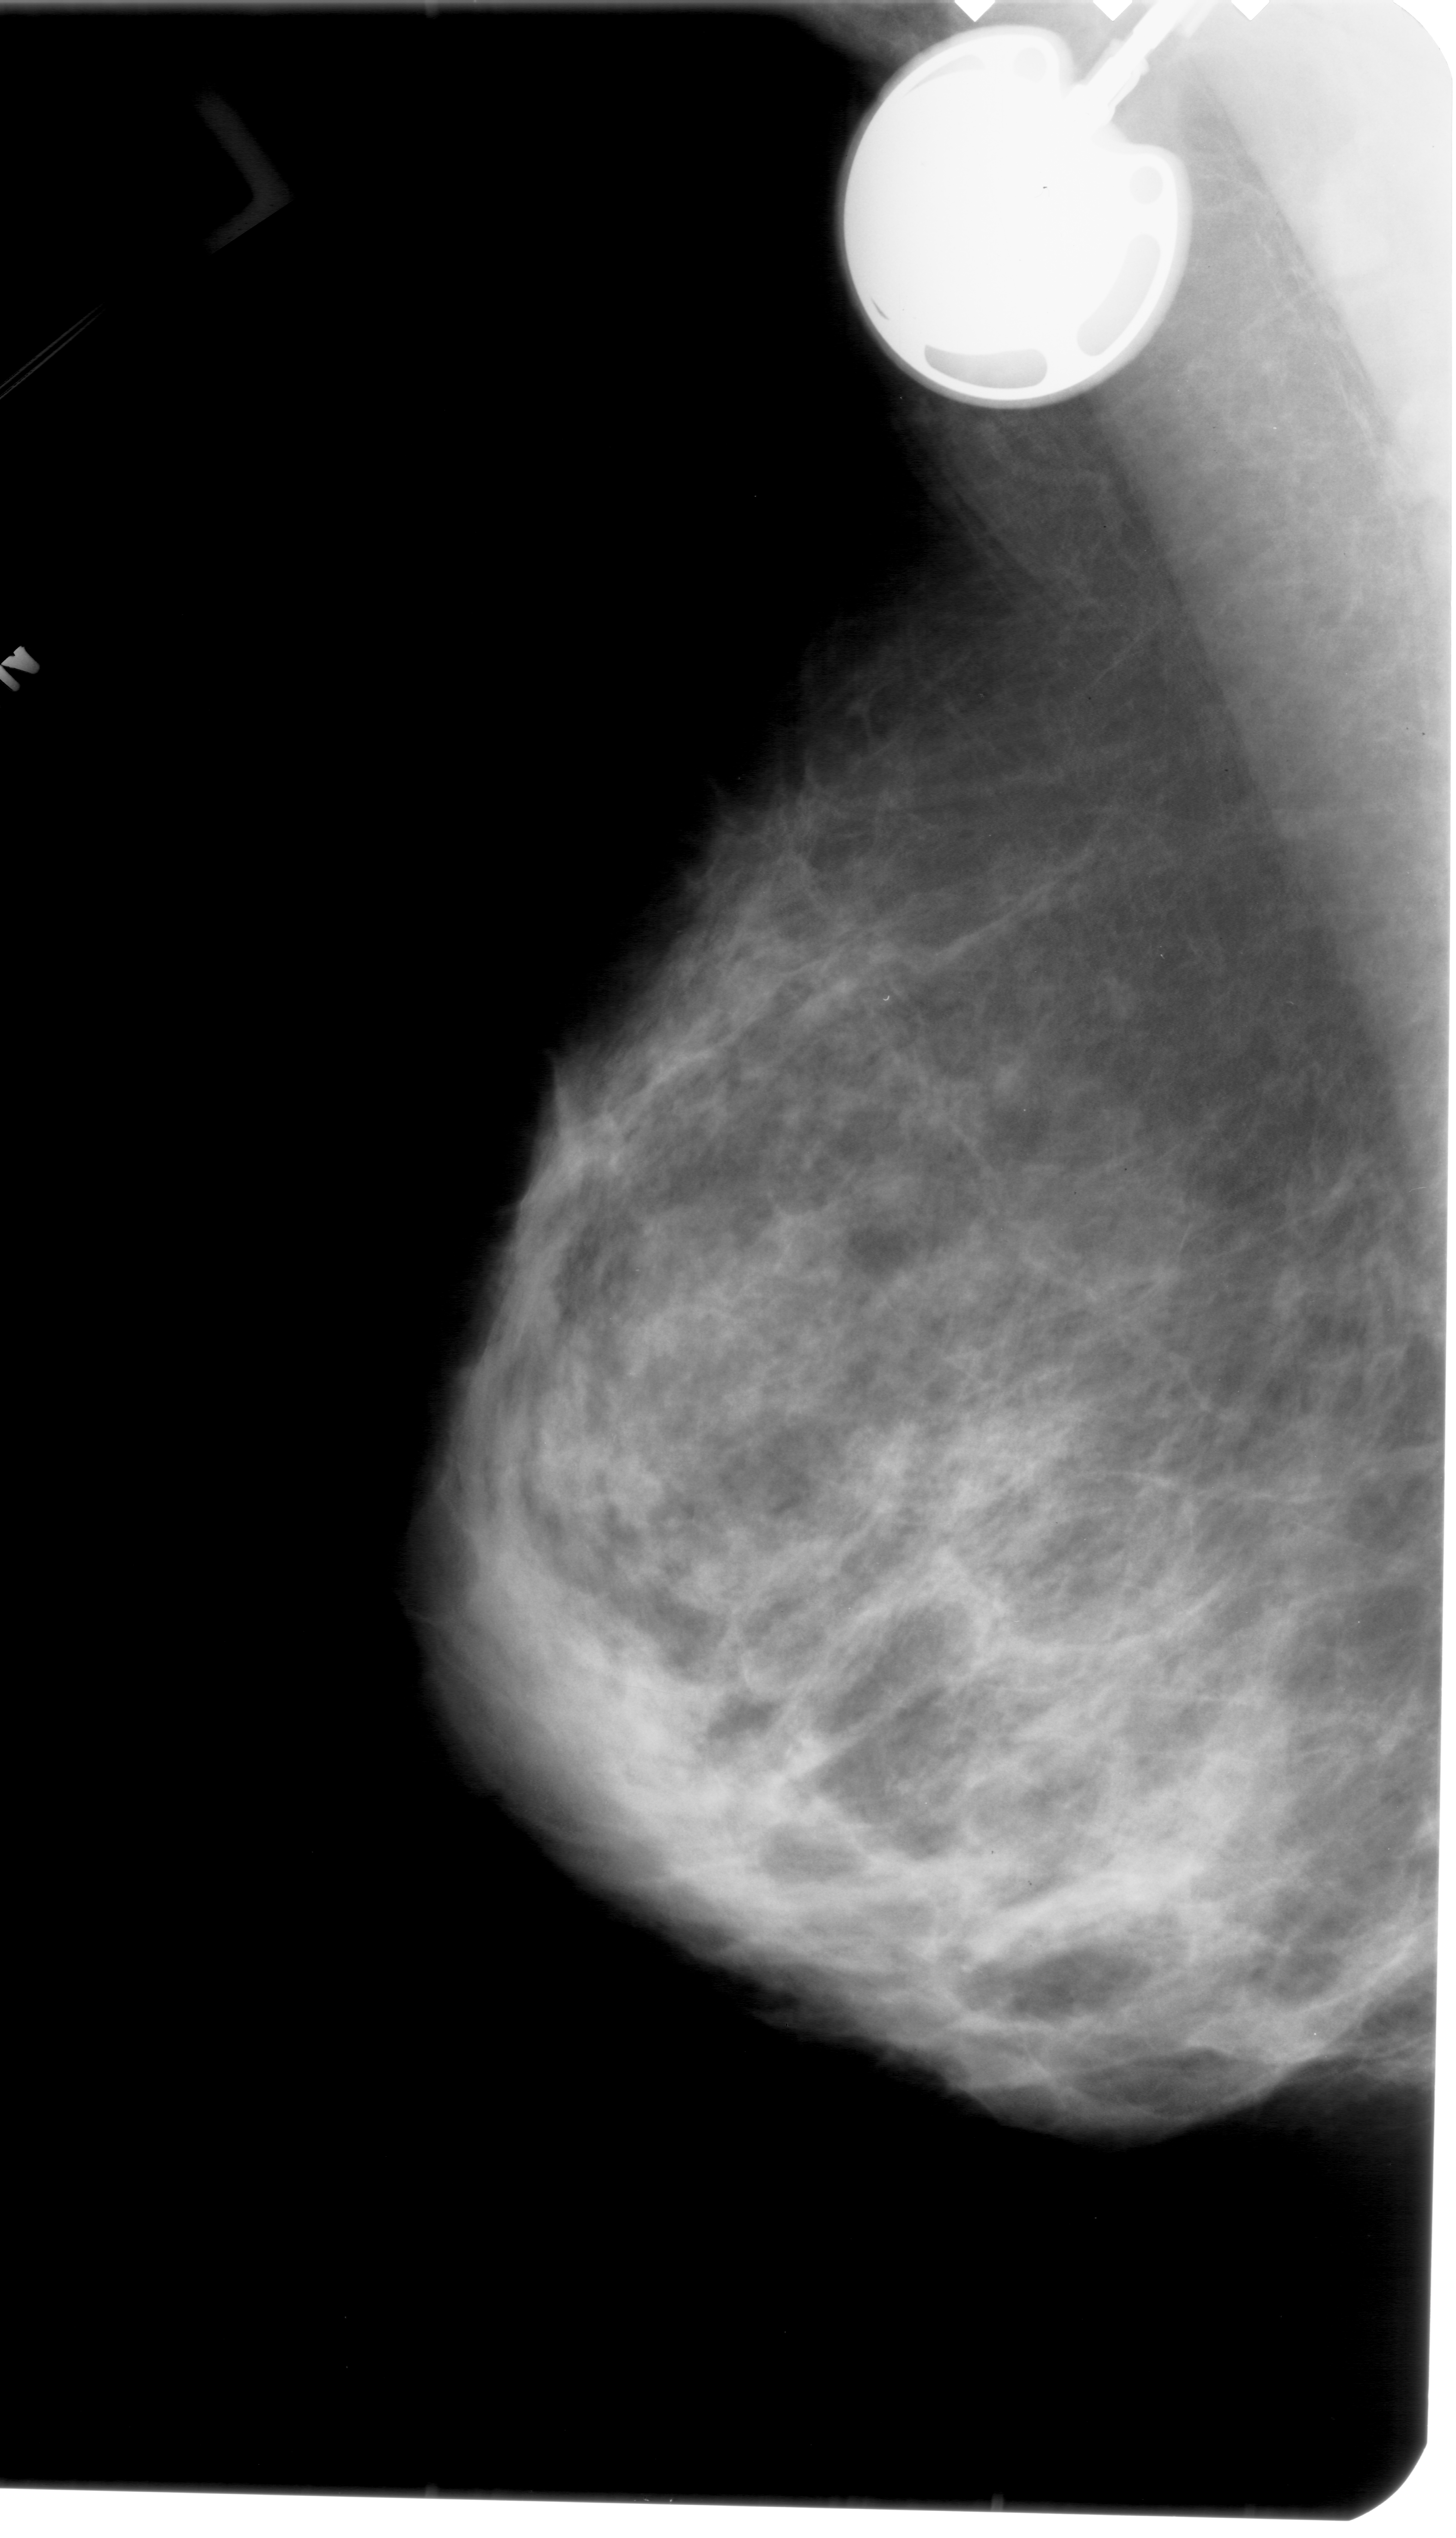
Scanned film-screen mammogram. Left breast. Mediolateral oblique (MLO) view. 1456 × 2538 image matrix.
Expert-marked regions of interest on this image (one box per marked abnormality):
- calcifications, morphology fine linear branching, distribution linear; BI-RADS assessment category 4; pathology result (as recorded, not read from the image): malignant: bounding box [x1, y1, x2, y2] px = [771, 1662, 831, 1744]